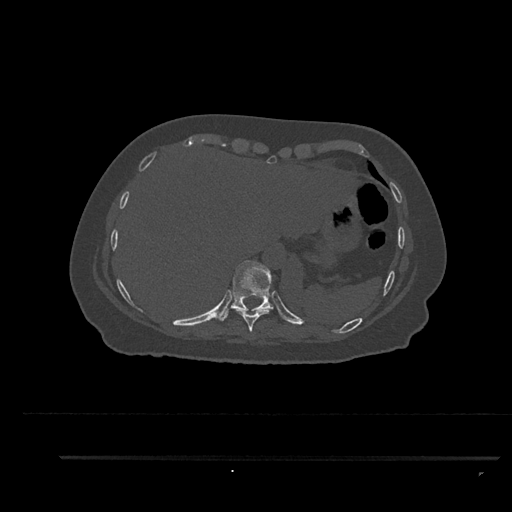
CT including the spine, one axial slice; slice 390 of 797 in the series (ordered by position); 120 kVp; bone window (W 1800 / L 400 HU); 0.5 mm slice thickness; 512 × 512 image matrix, field of view 408 × 408 mm. Female patient, age 44 years. From the clinical record (not read from this slice): primary cancer: renal; vertebrae with lytic lesions (as recorded): L1.
Structures marked on this image (semi-automatic segmentation, software-assisted and operator-edited):
- T10 vertebra: bounding box (x1, y1, x2, y2) in pixels: (216, 260, 274, 321)
- T9 vertebra: (236, 308, 273, 332)